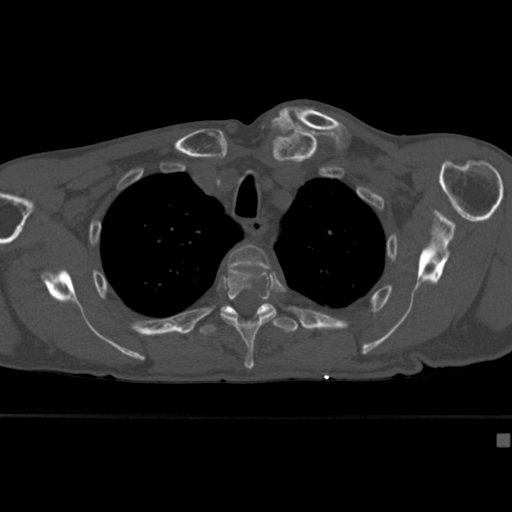
CT including the spine, one axial slice. Slice 320 of 430 in the series (ordered by position). Reconstruction kernel Br40s. Bone window (W 1800 / L 400 HU). 1.5 mm slice thickness. 512 × 512 image matrix. Male patient, age 64 years. Case-level facts recorded for this patient, not image findings: primary cancer: uterus; vertebrae with lytic lesions (as recorded): T1, T4, T5, T7, L5.
Annotated regions visible in this slice (semi-automatically segmented with operator editing):
- T3 vertebra: bounding box (x1, y1, x2, y2) in pixels: (227, 244, 271, 270)
- T4 vertebra: (219, 270, 282, 370)
- T5 vertebra: (199, 303, 298, 335)